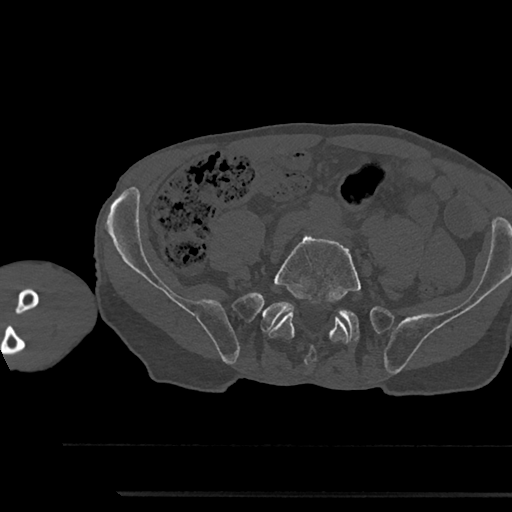
CT including the spine, one axial slice. Position 332 of 797 along the scan axis. 120 kVp. Bone window (W 1800 / L 400 HU). 512 × 512 image matrix, field of view 367 × 367 mm. Male patient, age 79 years. From the clinical record (not read from this slice): primary cancer: prostate.
Annotated regions visible in this slice (semi-automatic segmentation, software-assisted and operator-edited):
- L5 vertebra: bounding box [x1, y1, x2, y2] px = [268, 235, 361, 365]